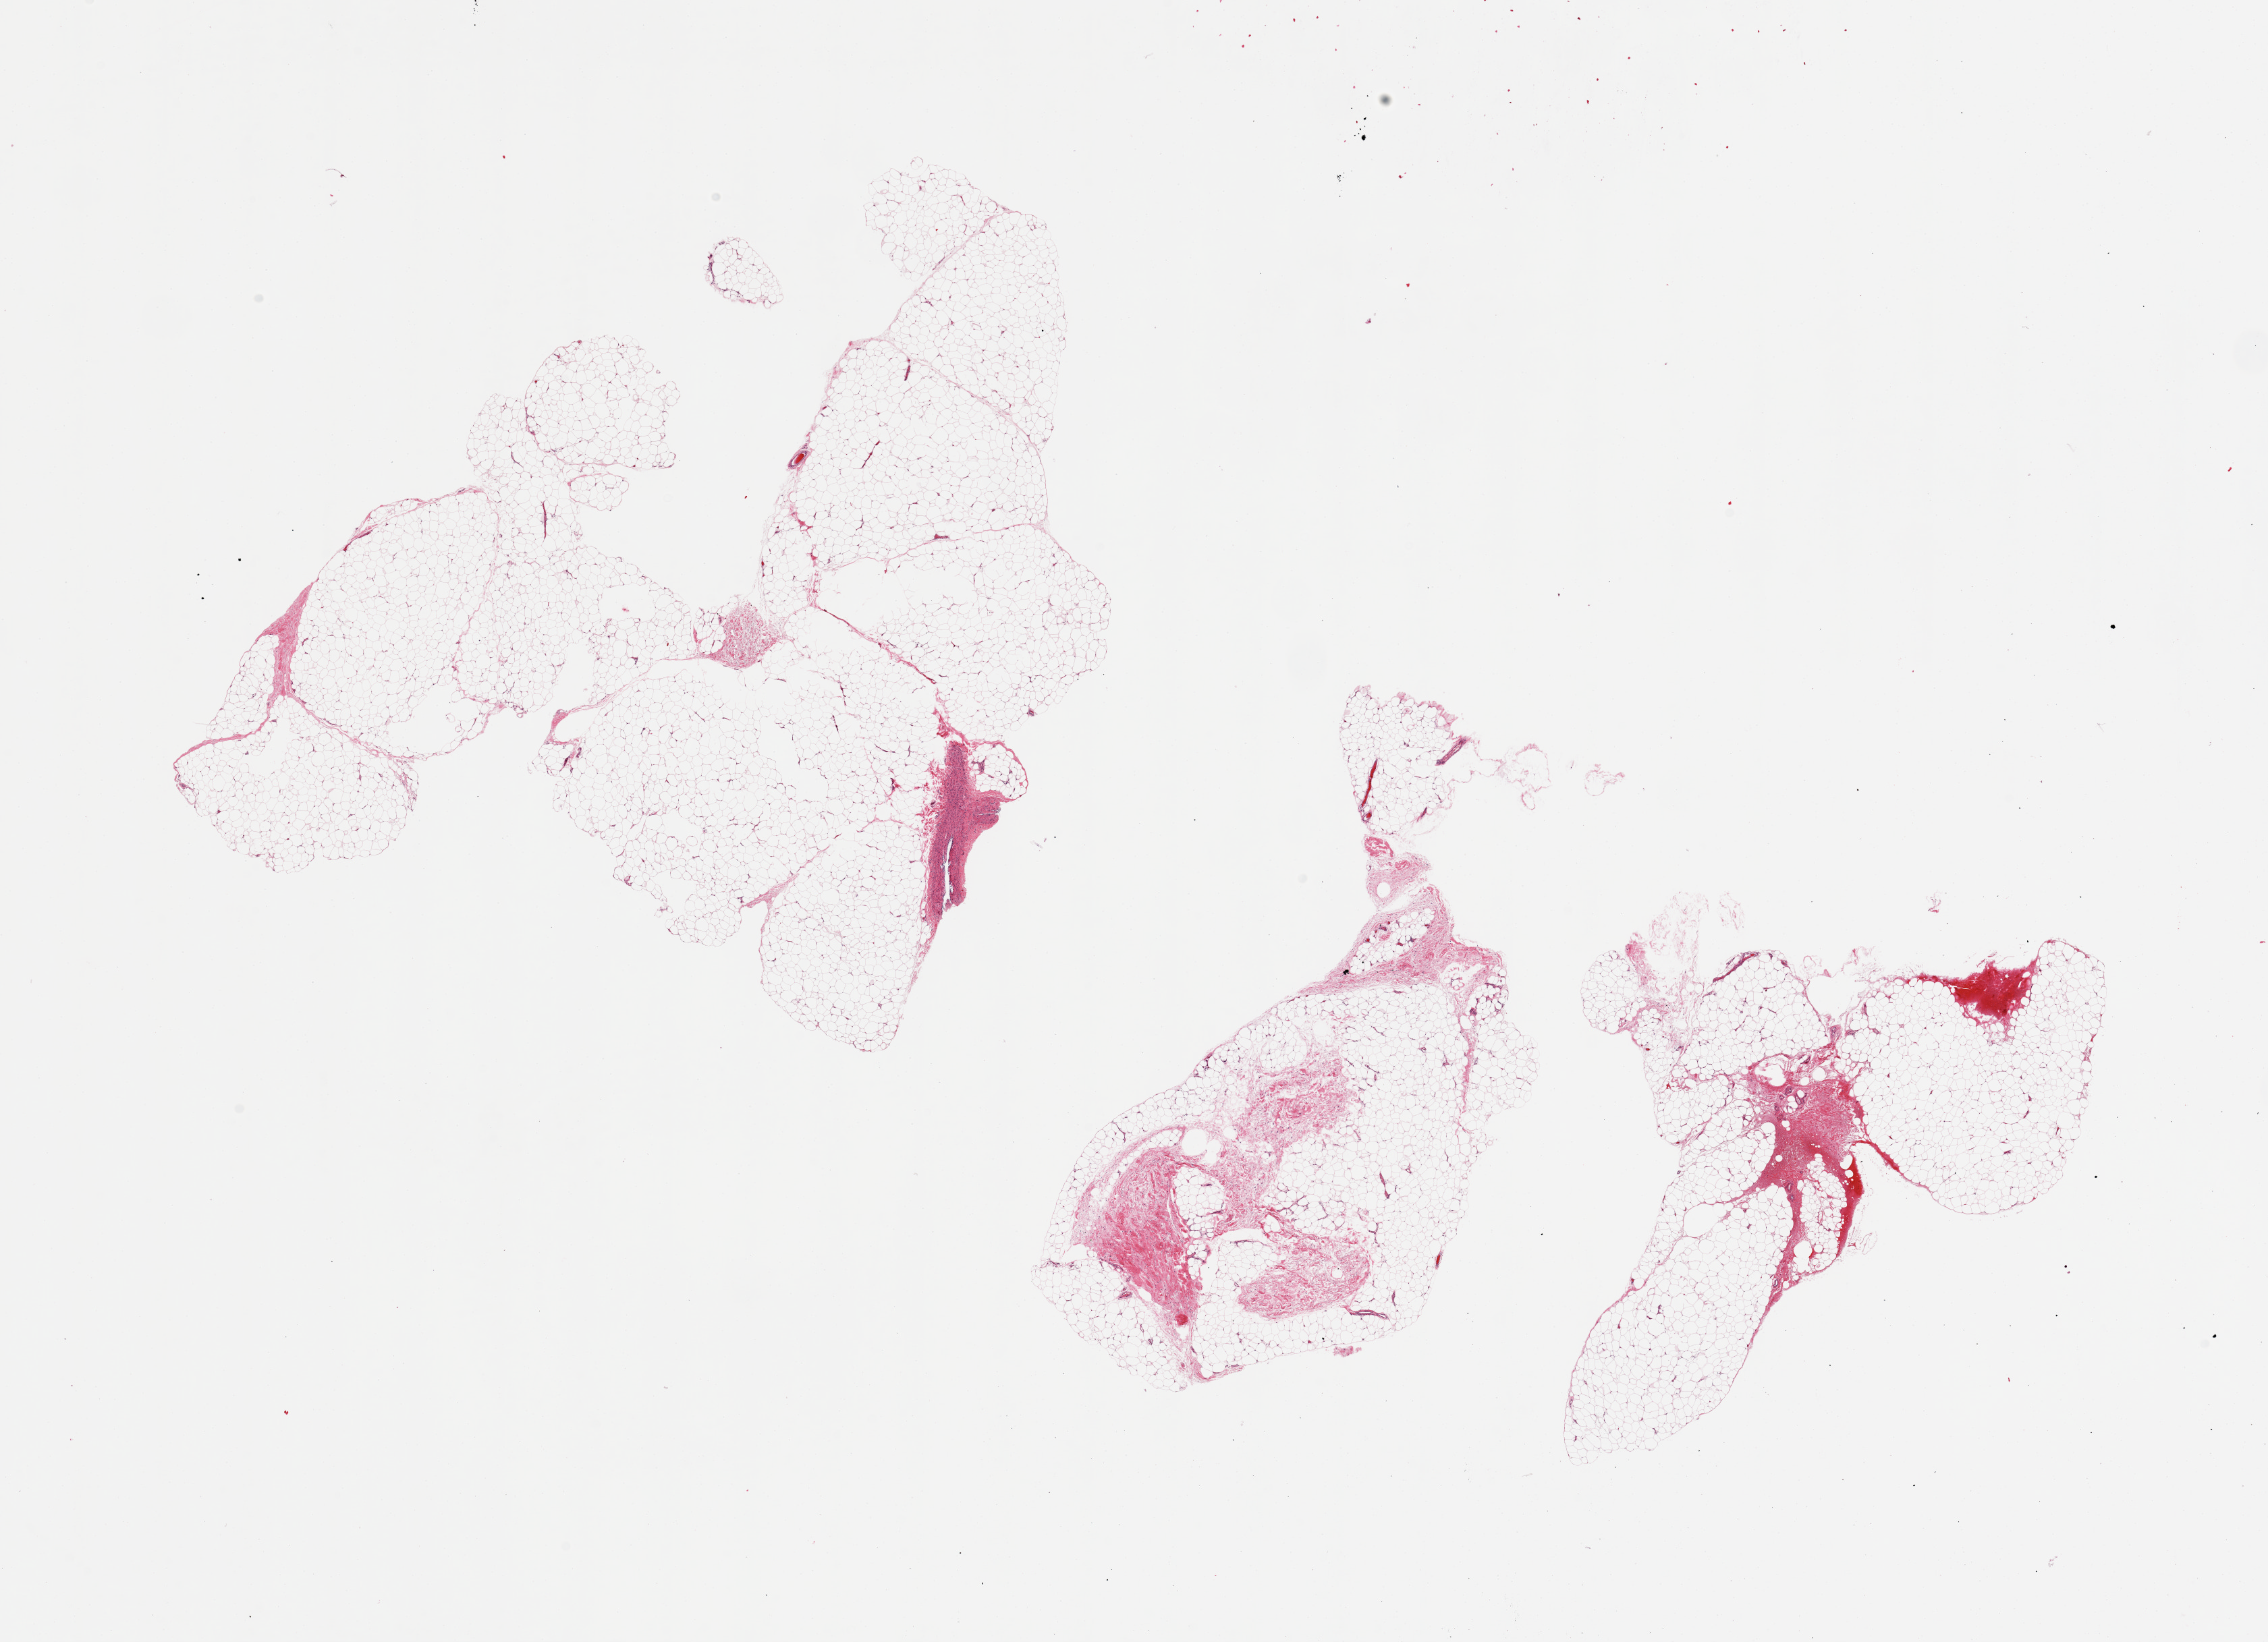
Haematoxylin and eosin whole-slide image — whole scanned area (about 26.6 x 19.2 mm) shown as a low-resolution overview, PAXgene-fixed, paraffin-embedded tissue, sampled site (target tissue): adipose tissue, donor tissue sample. Donor: male.
Reviewer comment on this tissue sample: 3 pieces.